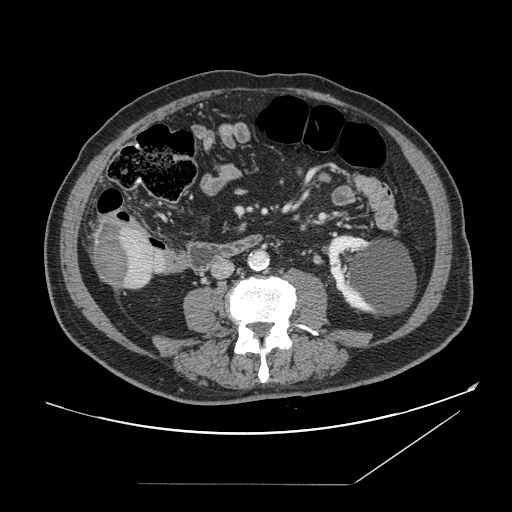
Contrast-enhanced abdominal CT, one axial slice. Position 31 of 166 along the scan axis. Soft-tissue window (W 400 / L 40 HU). 2.5 mm slice thickness. 512 × 512 image matrix, field of view 416 × 416 mm. Male patient, age 80 years. From the clinical record (not read from this slice): diagnosis: colorectal cancer liver metastases, imaged before liver resection; multiple liver metastases: no; largest metastasis: 2.2 cm.
Structures marked on this image (expert manual segmentation):
- liver: bounding box <91,221,158,290> (left, top, right, bottom; pixels)
- liver metastasis: <94,225,132,287>